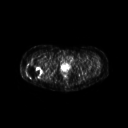
FDG PET of an extremity soft-tissue mass (from a PET/CT study), one axial slice; slice 43 of 267 in the series (ordered by position); 128 × 128 image matrix. Patient: female, 57 years. Case-level facts recorded for this patient, not image findings: histological type: epithelioid sarcoma with vascular differentiation; site of the primary tumour: right buttock.
Structures marked on this image (expert contour drawn on MRI and transferred to this co-registered scan by the dataset authors):
- gross tumour volume (mass): bounding box <24,61,43,80> (left, top, right, bottom; pixels)